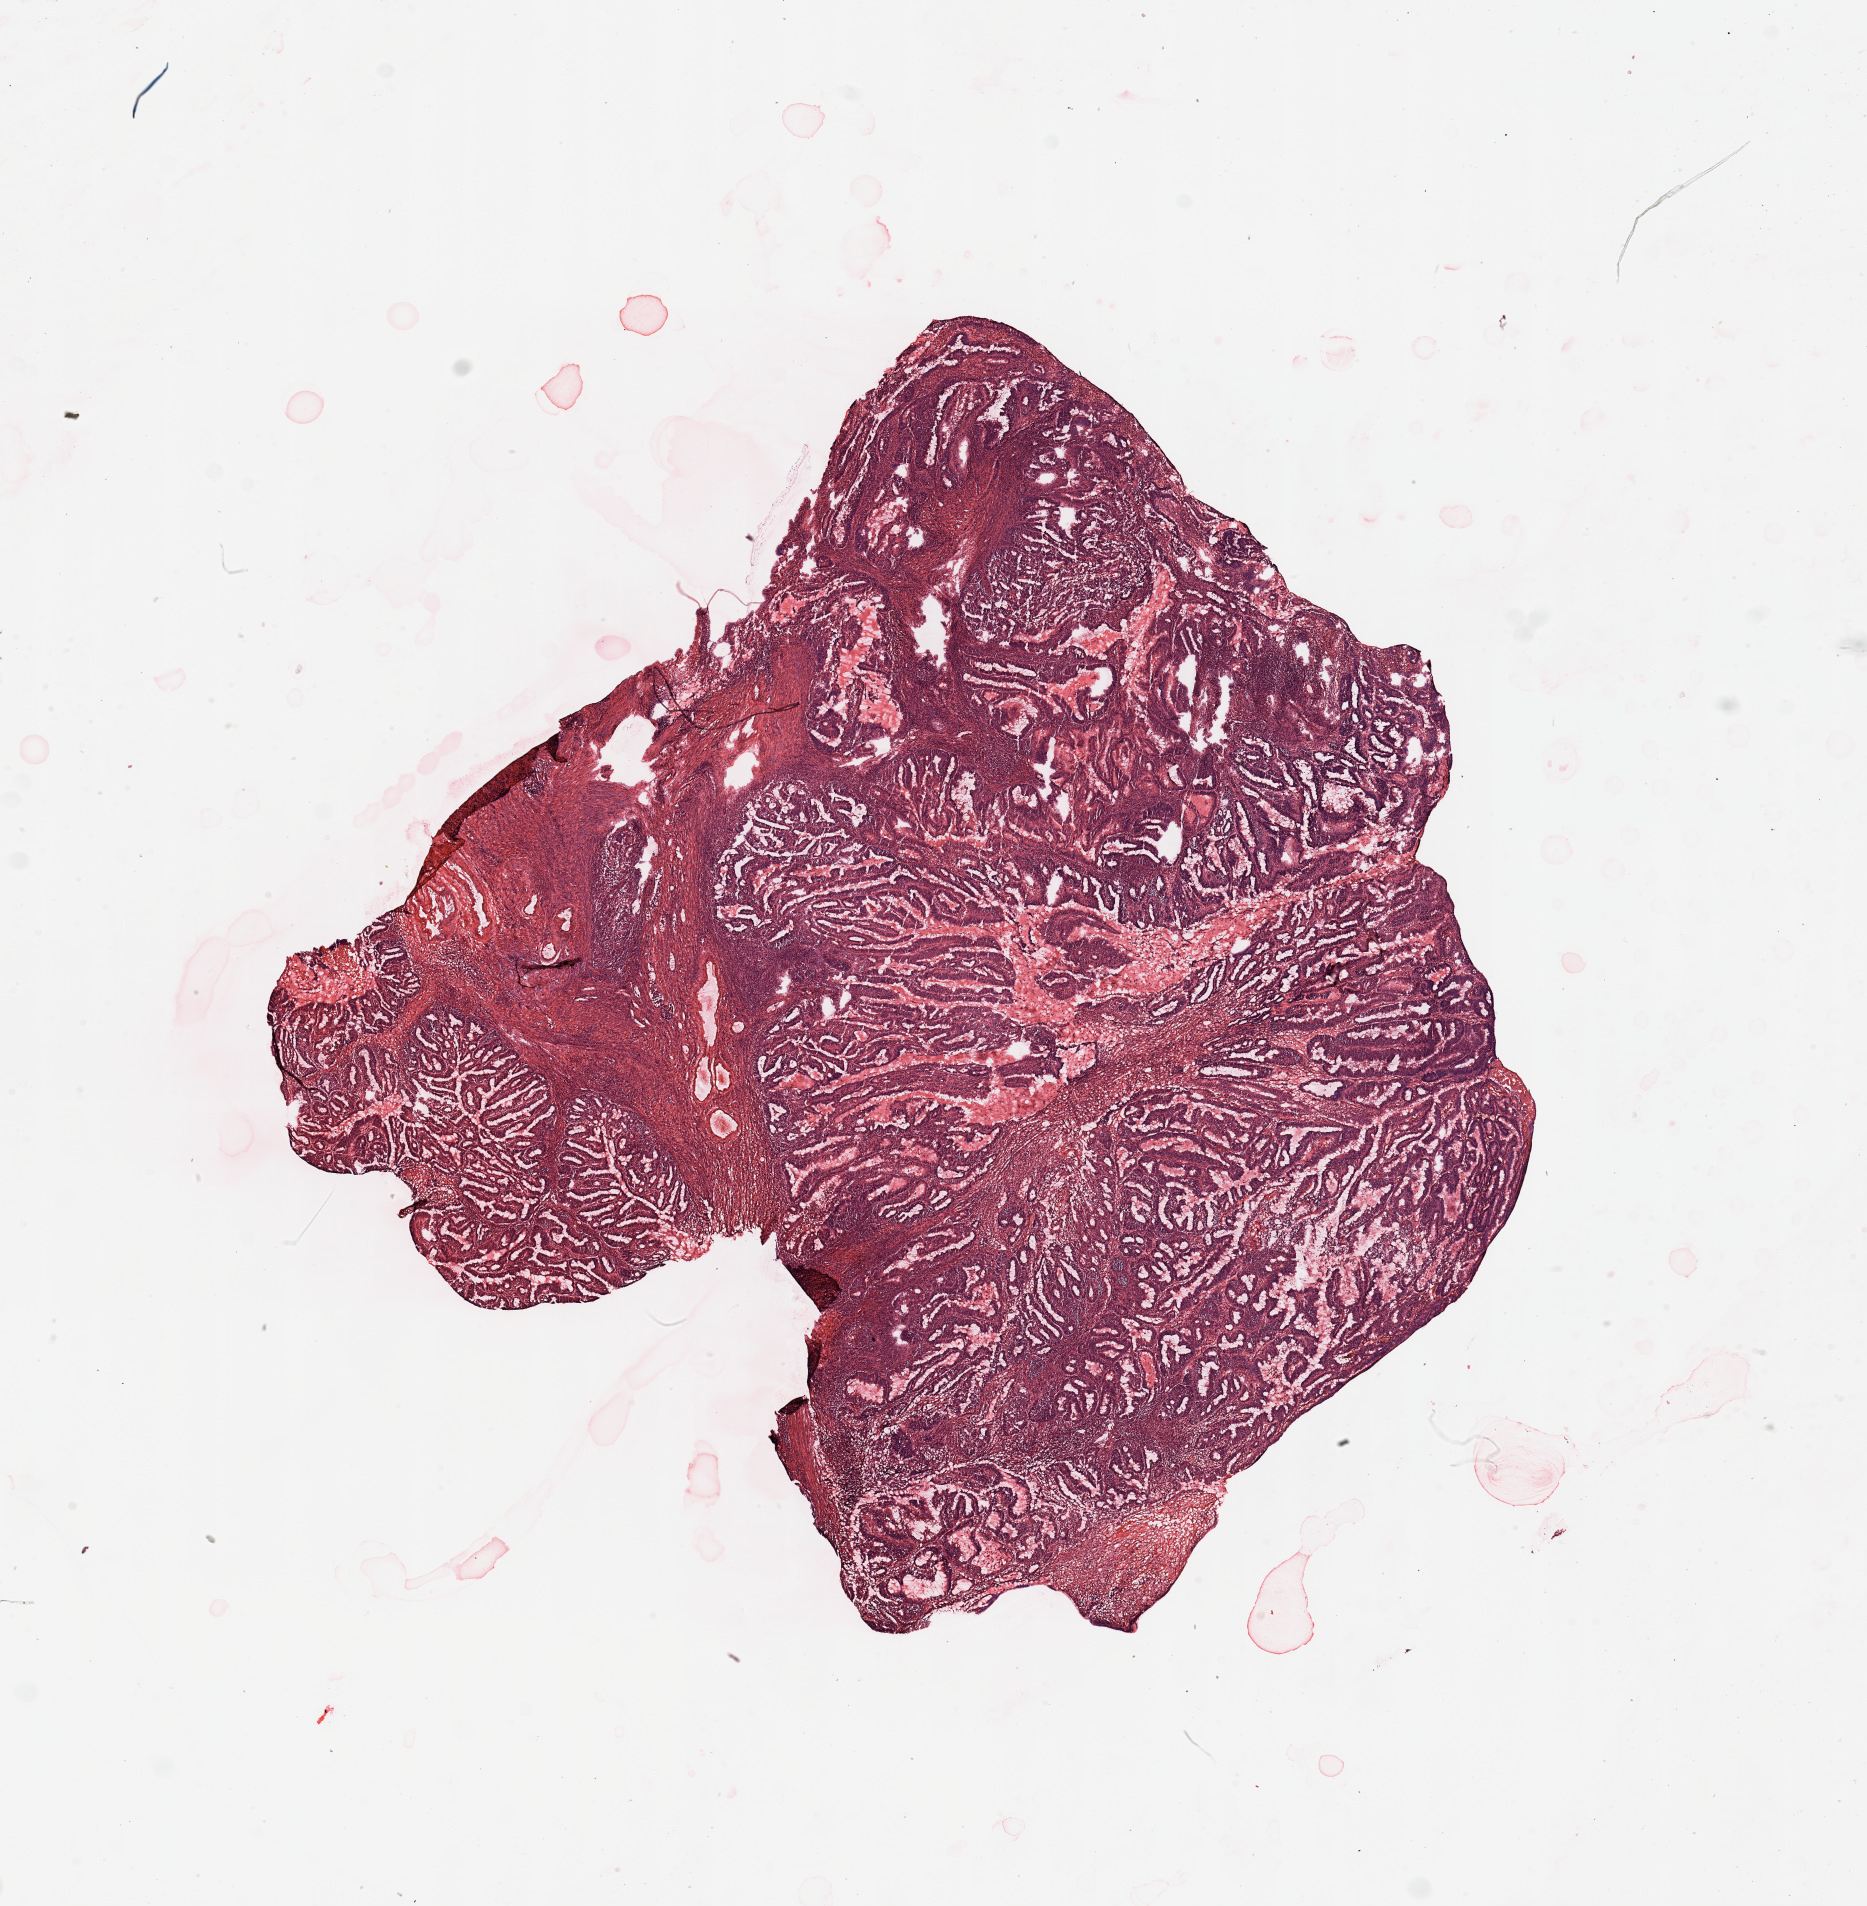
H&E-stained whole-slide image, a low-resolution overview of the entire scanned area, about 14.8 x 15.1 mm (from a 20x scan). Tumour tissue sample, sampled site: uterus. Patient: female, age 65 years. Histologic grade: G2 (moderately differentiated). Composition of this section per pathologist review: tumour nuclei 80%, necrosis 0%.
* AJCC pathologic stage: I
* diagnosis: Endometrioid adenocarcinoma, NOS